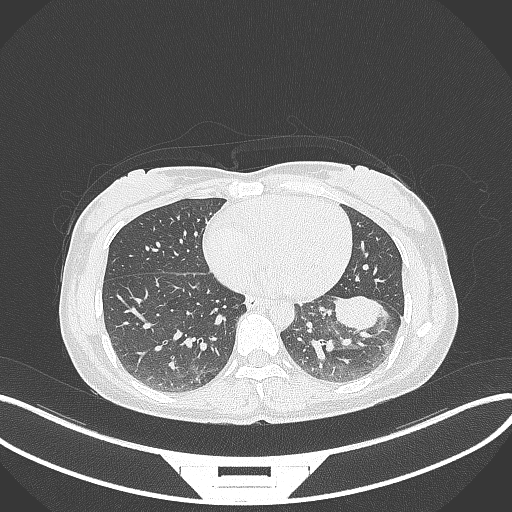
Chest CT, one axial slice; slice 18 of 244 in the series (ordered by position); 120 kVp; lung window (W 1500 / L -600 HU); 512 × 512 image matrix, field of view 400 × 400 mm. Patient: female, 41 years. Case-level facts recorded for this patient, not image findings: clinical TNM (as recorded): T2a N3 M1b.
Structures marked on this image (rectangle marked by the reading radiologist):
- lung tumour (recorded histology: adenocarcinoma): box from (x=330, y=289) to (x=387, y=333) px